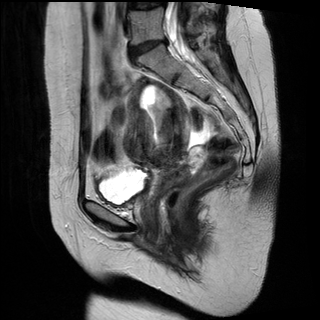
Pelvic MRI for cervical cancer, one sagittal slice. Position 18 of 34 along the scan axis. T2-weighted. 1.5 T. TE 89 ms, TR 3320 ms. 4 mm slice thickness. 320 × 320 image matrix, field of view 260 × 260 mm. Patient: female, 49 years.
Outlined on this slice (manually delineated by an expert):
- uterus and cervix: bounding box [x1, y1, x2, y2] px = [122, 78, 191, 201]